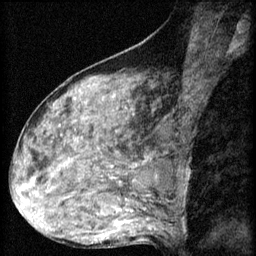
Breast MRI (dynamic contrast-enhanced), one sagittal slice. Position 29 of 60 along the scan axis. 3 images stored at this slice position (order not interpretable as contrast timing). 1.5 T. TE 4.2 ms, TR 8.2 ms. 2 mm slice thickness. 256 × 256 image matrix, field of view 180 × 180 mm. Female patient, age 48 years.
Outlined on this slice (semi-automatically segmented with operator editing):
- analysis volume of interest (the breast-tissue region the enhancement analysis was run in; not a lesion): bounding box <48,160,125,217> (left, top, right, bottom; pixels)
- tumour enhancement mask (voxels above the 70 % enhancement threshold inside the analysis volume of interest): <97,166,113,215>